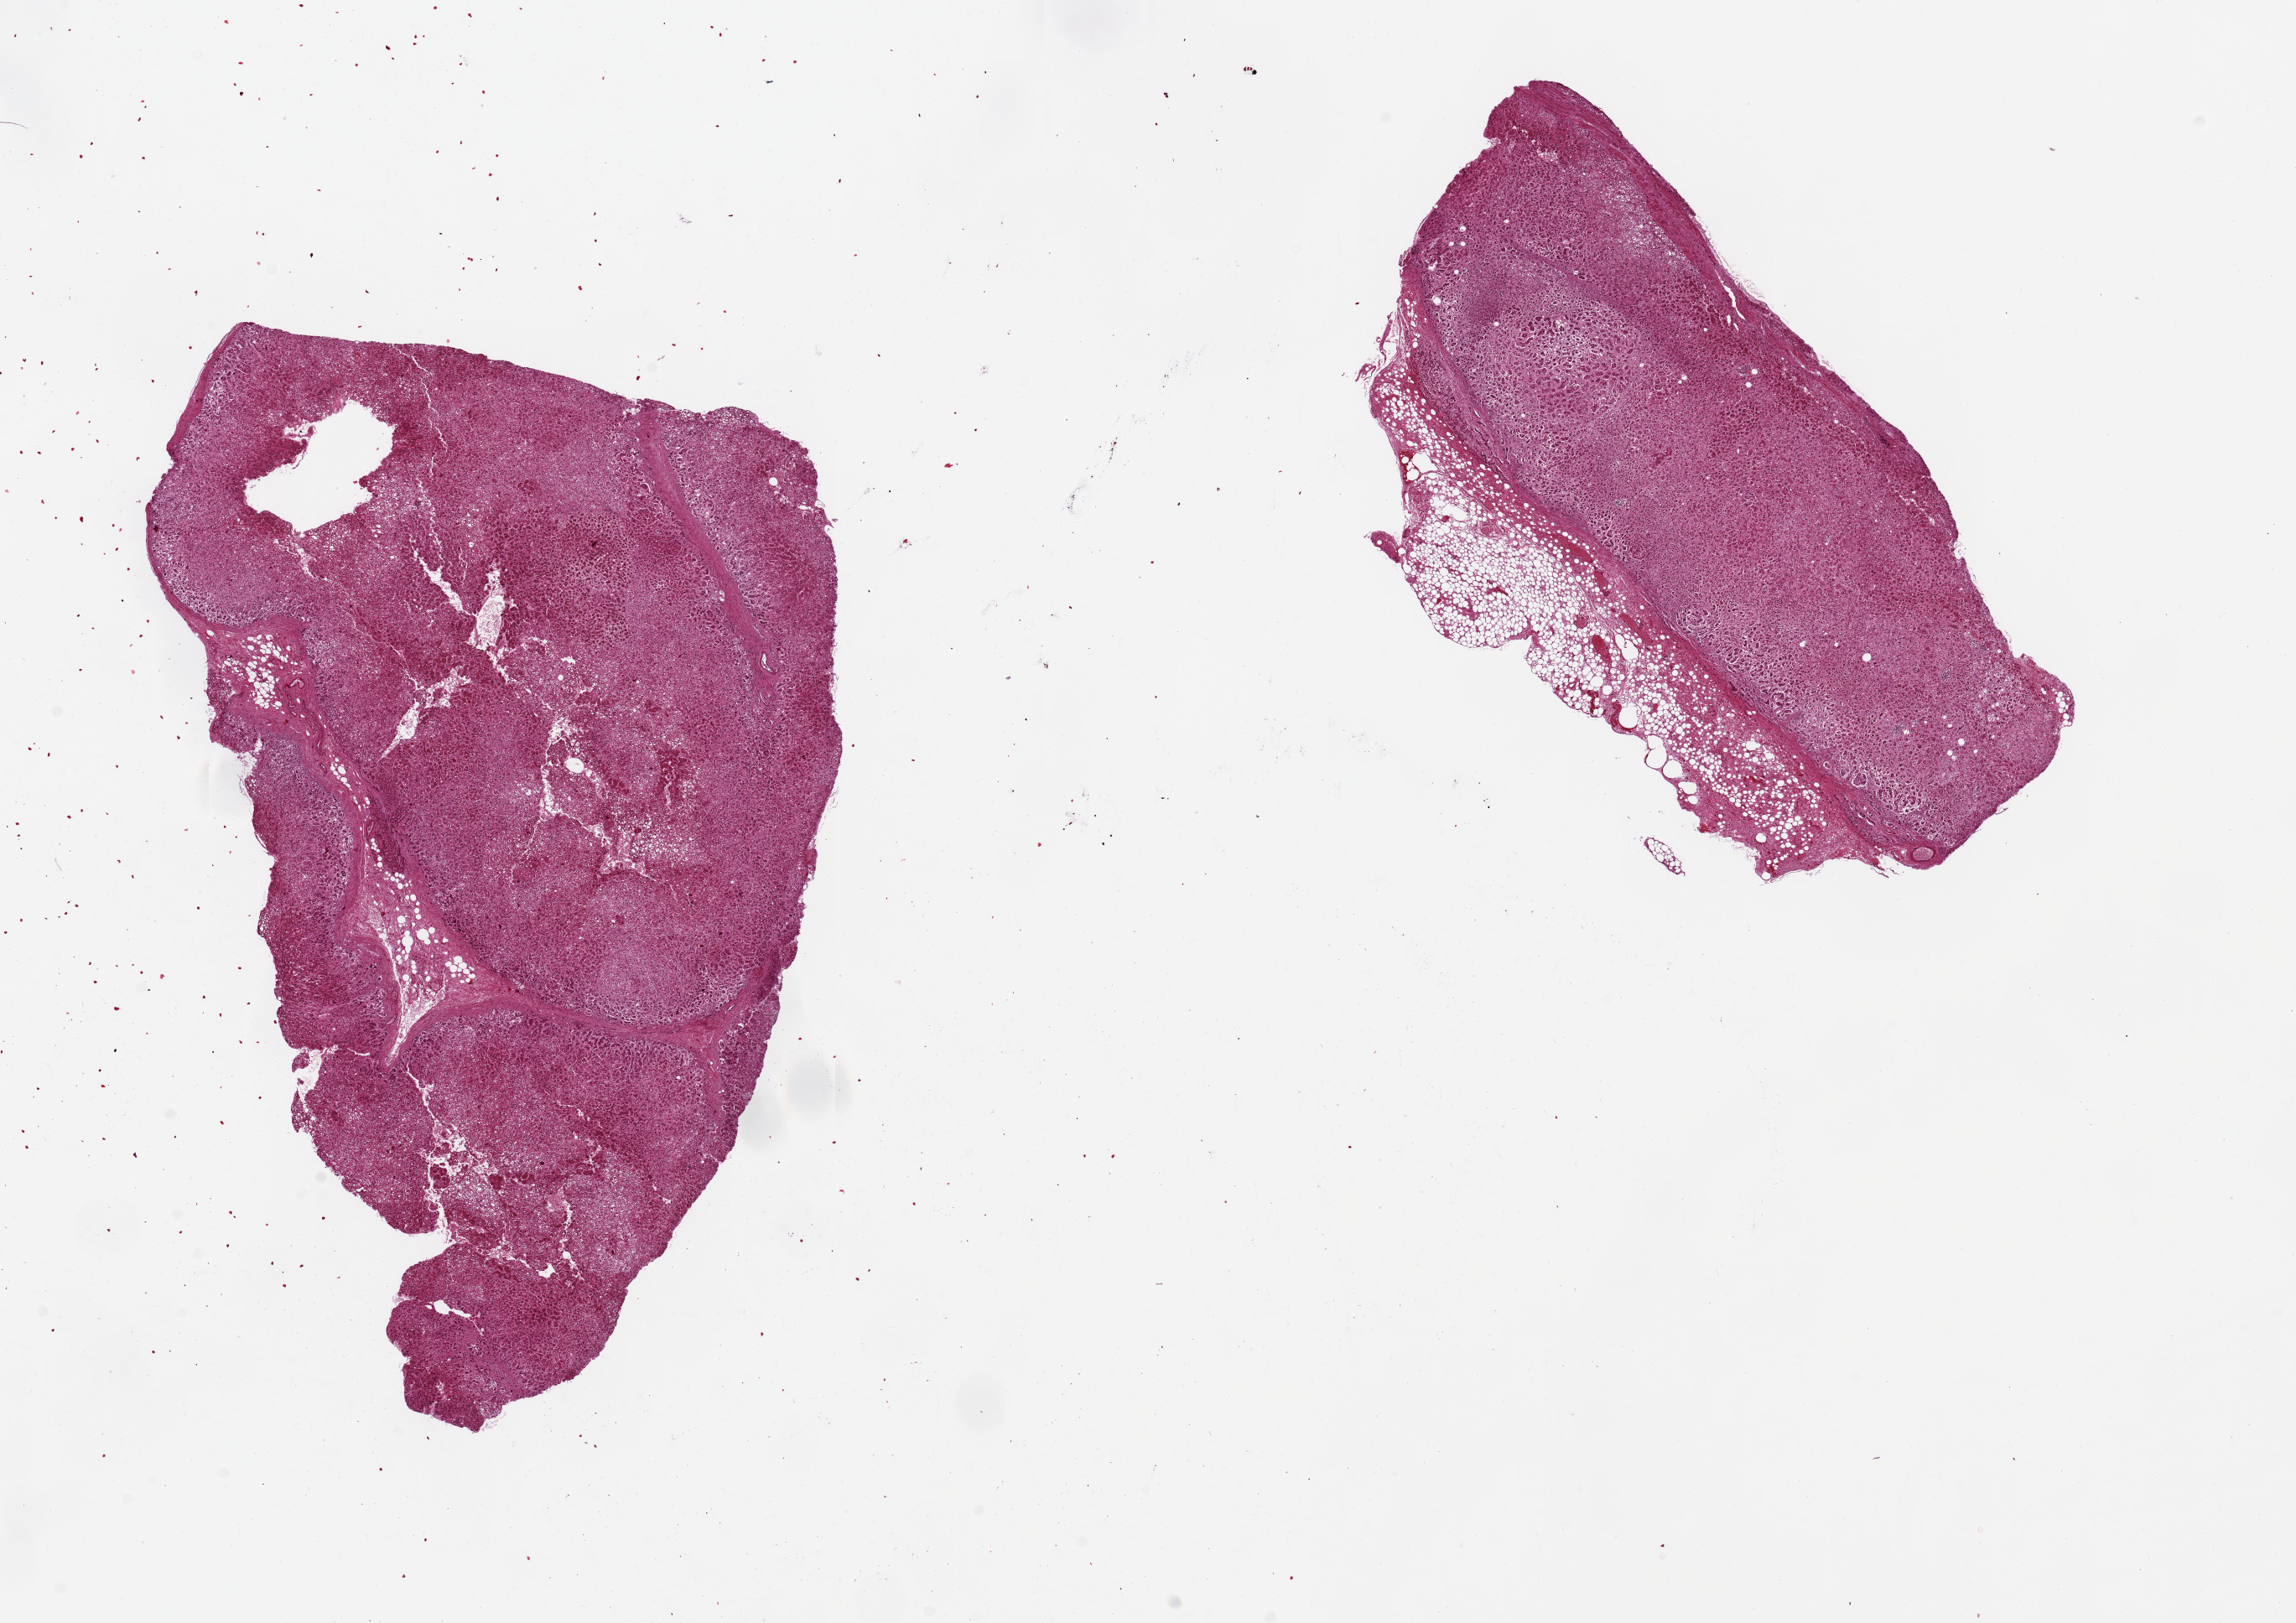
Whole-slide image, H&E stain, brightfield — shown as a low-resolution overview of the whole scanned area (about 21.7 x 15.3 mm). PAXgene-fixed, paraffin-embedded tissue. Target tissue: adrenal gland. Donor tissue sample. Male donor.
• pathologist's review note for this sample: 2 pieces, 11x7 & 4x1mm; 1.5 mm adipose along long edge of smaller piece